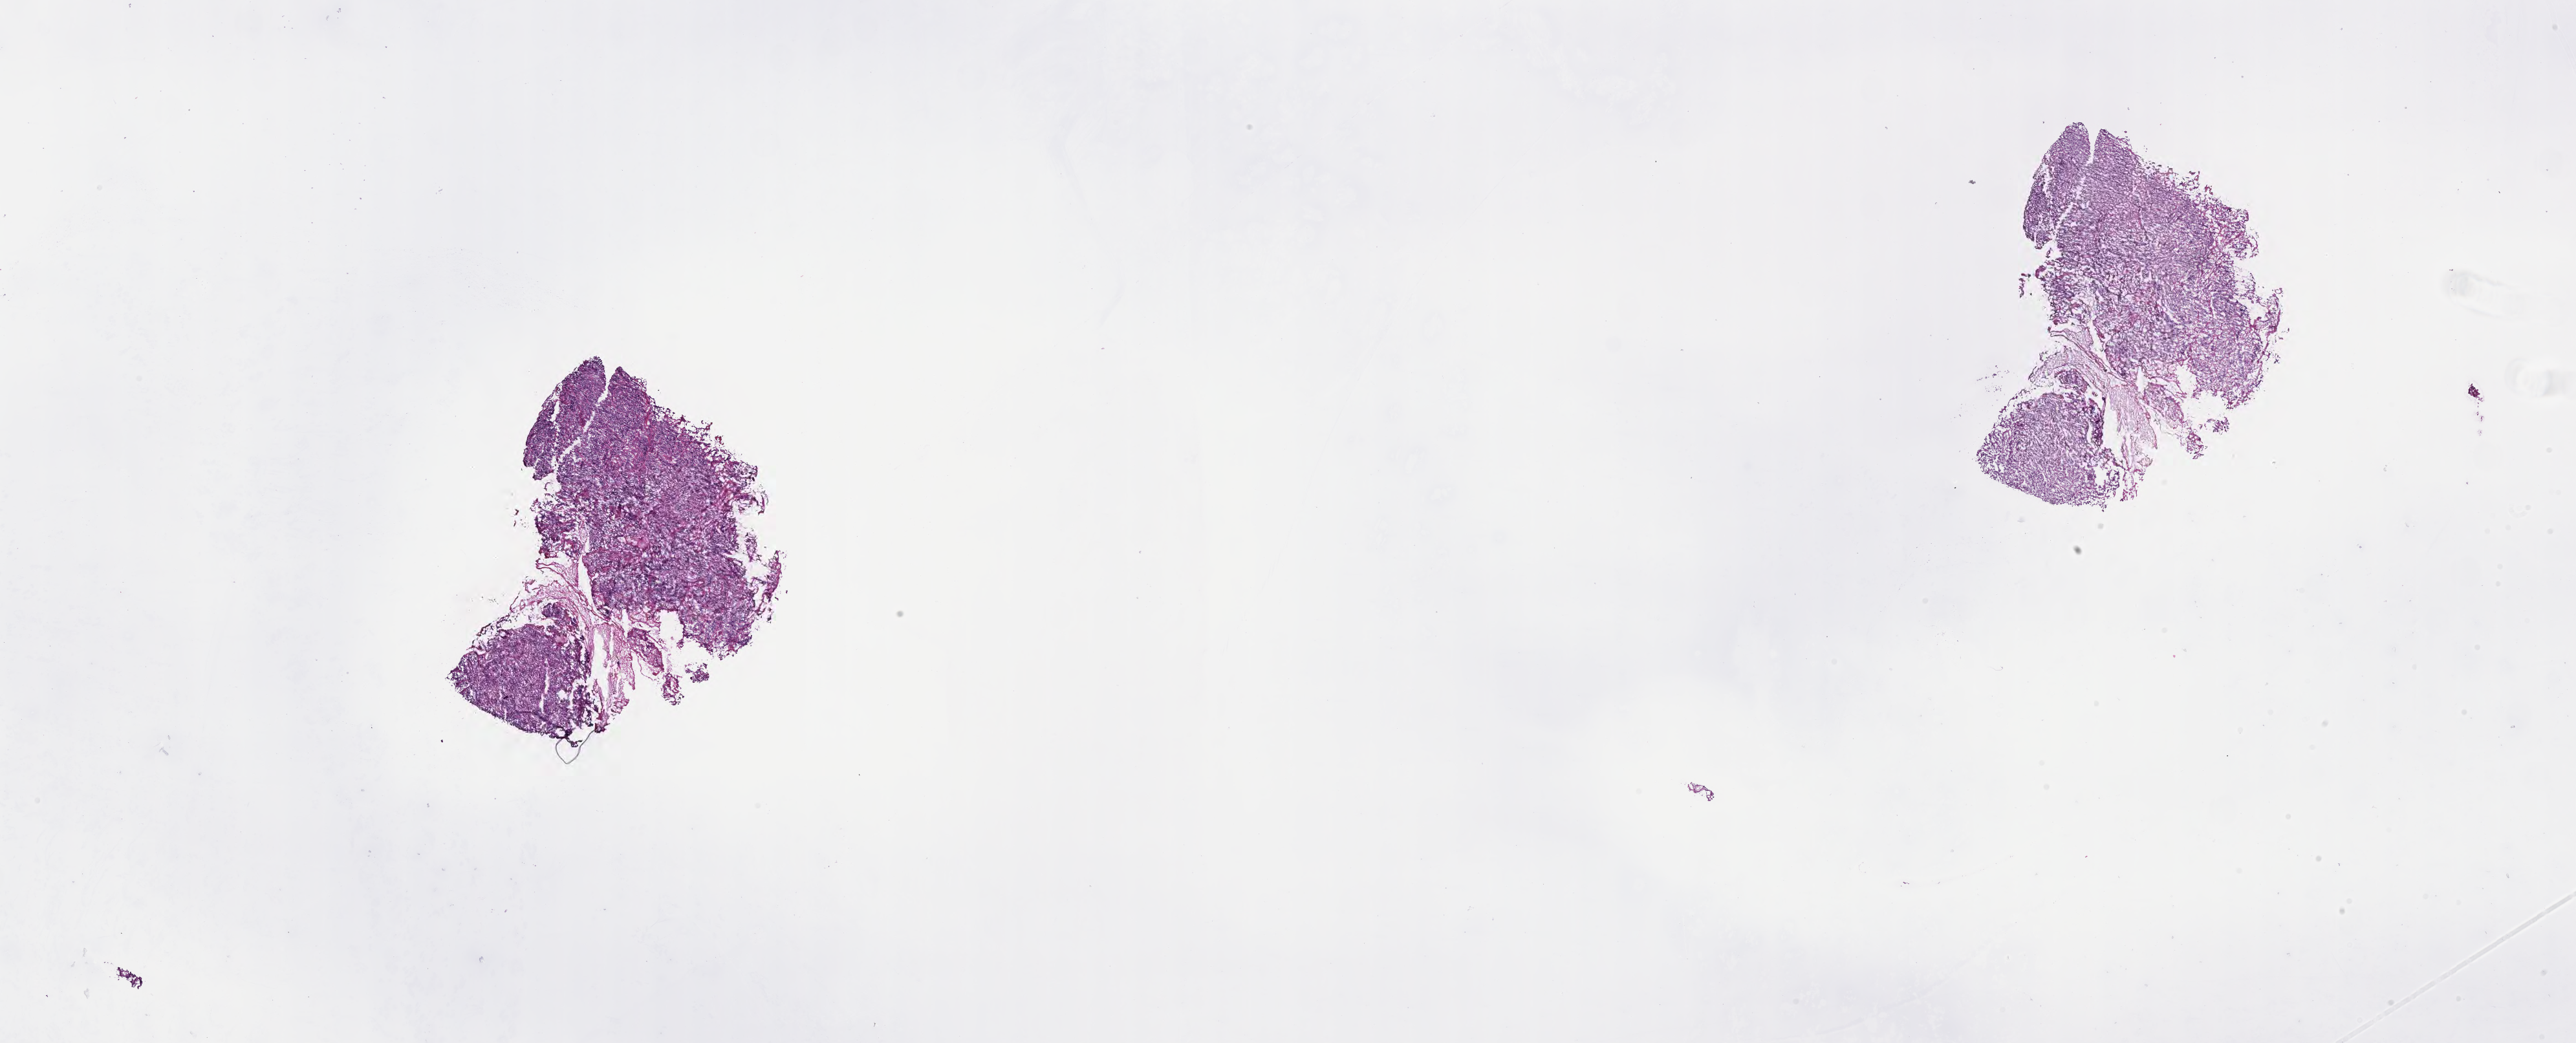
Digitized haematoxylin and eosin-stained section of tumor tissue from the nasopharynx — shown as a low-resolution overview of the whole scanned area (about 32.2 x 13.0 mm). Cryosection (OCT / tissue freezing medium). Male patient, age 167 months (13 years 11 months).
Diagnosis: Neoplasm, uncertain whether benign or malignant.